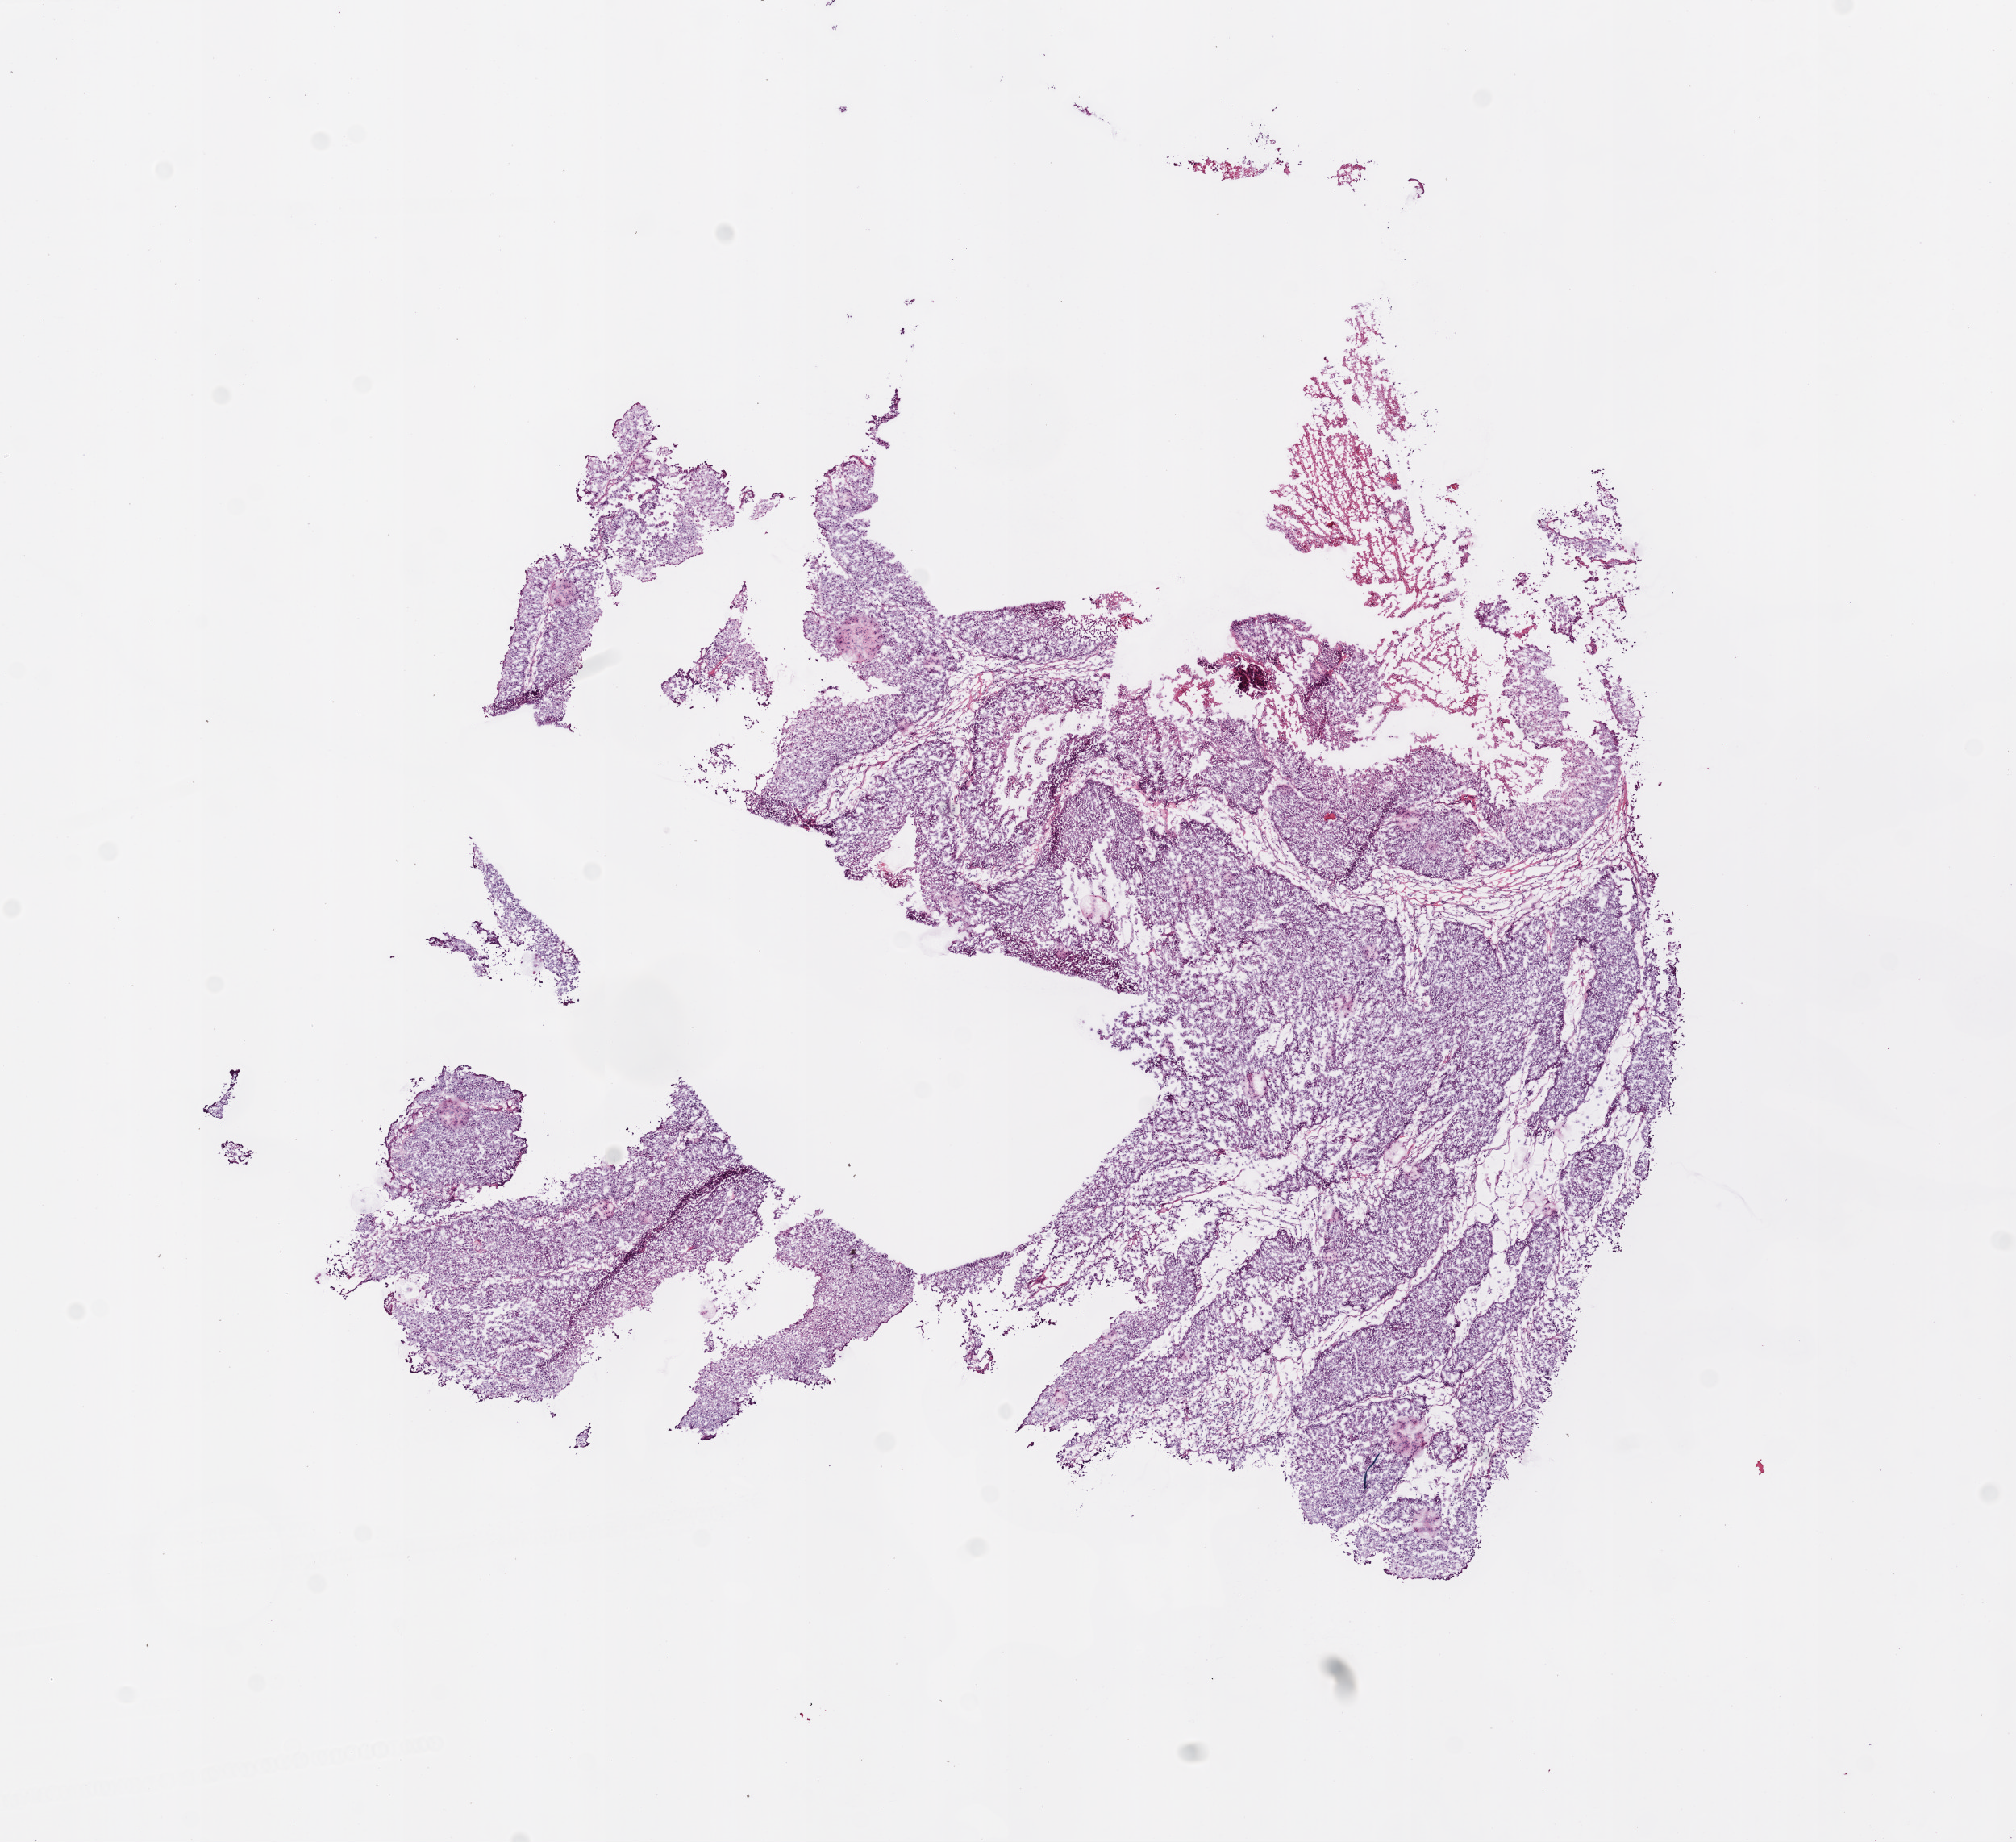
Digitized Hematoxylin and eosin (H&E) stained tissue section (whole slide) — whole scanned area (about 10.0 x 9.2 mm) shown as a low-resolution overview, frozen section from the bottom of the tissue portion, recurrent tumour sample from the ovary. Female, age 61 years at initial diagnosis.
This section: recurrent tumour. Patient diagnosis: Serous cystadenocarcinoma, NOS.